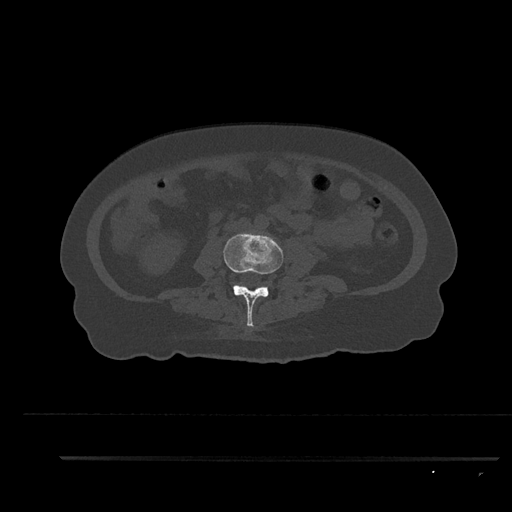
CT including the spine, one axial slice. Position 72 of 797 along the scan axis. Reconstruction kernel Br40s/3. 120 kVp. Bone window (W 1800 / L 400 HU). 0.5 mm slice thickness. 512 × 512 image matrix, field of view 408 × 408 mm. Patient: female, 44 years. Case-level facts recorded for this patient, not image findings: primary cancer: renal; vertebrae with lytic lesions (as recorded): L1.
Structures marked on this image (semi-automatic segmentation, software-assisted and operator-edited):
- L3 vertebra: box from (x=223, y=232) to (x=284, y=327) px